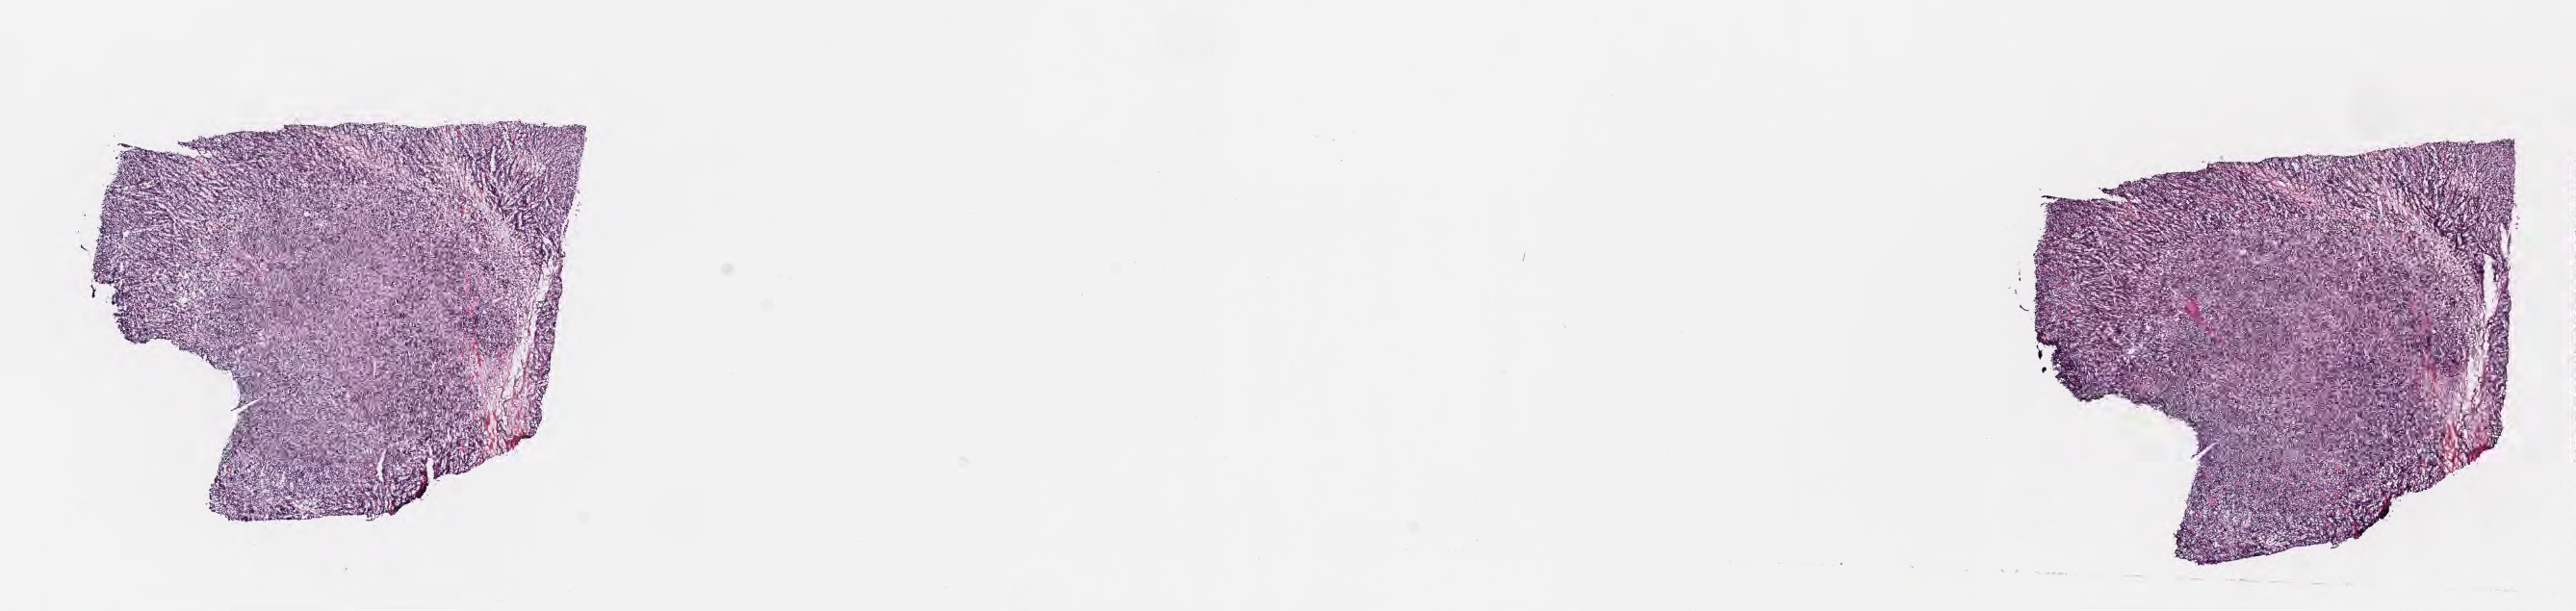
H&E whole-slide image — a low-resolution overview of the entire scanned area, about 21.6 x 5.1 mm, cryosection, primary tumor, site: colon. Female patient, 12 years old. Composition of this section per pathologist review: tumor cells 90%, tumor nuclei 95%, stromal cells 5%, necrosis 5%, normal cells 0%. Inflammatory infiltration, as recorded: lymphocyte infiltration 40%, monocyte infiltration 25%, neutrophil infiltration 10%.
- section: top of the tissue portion
- histologic diagnosis: Burkitt lymphoma, NOS
- Ann Arbor stage (patient): Stage III